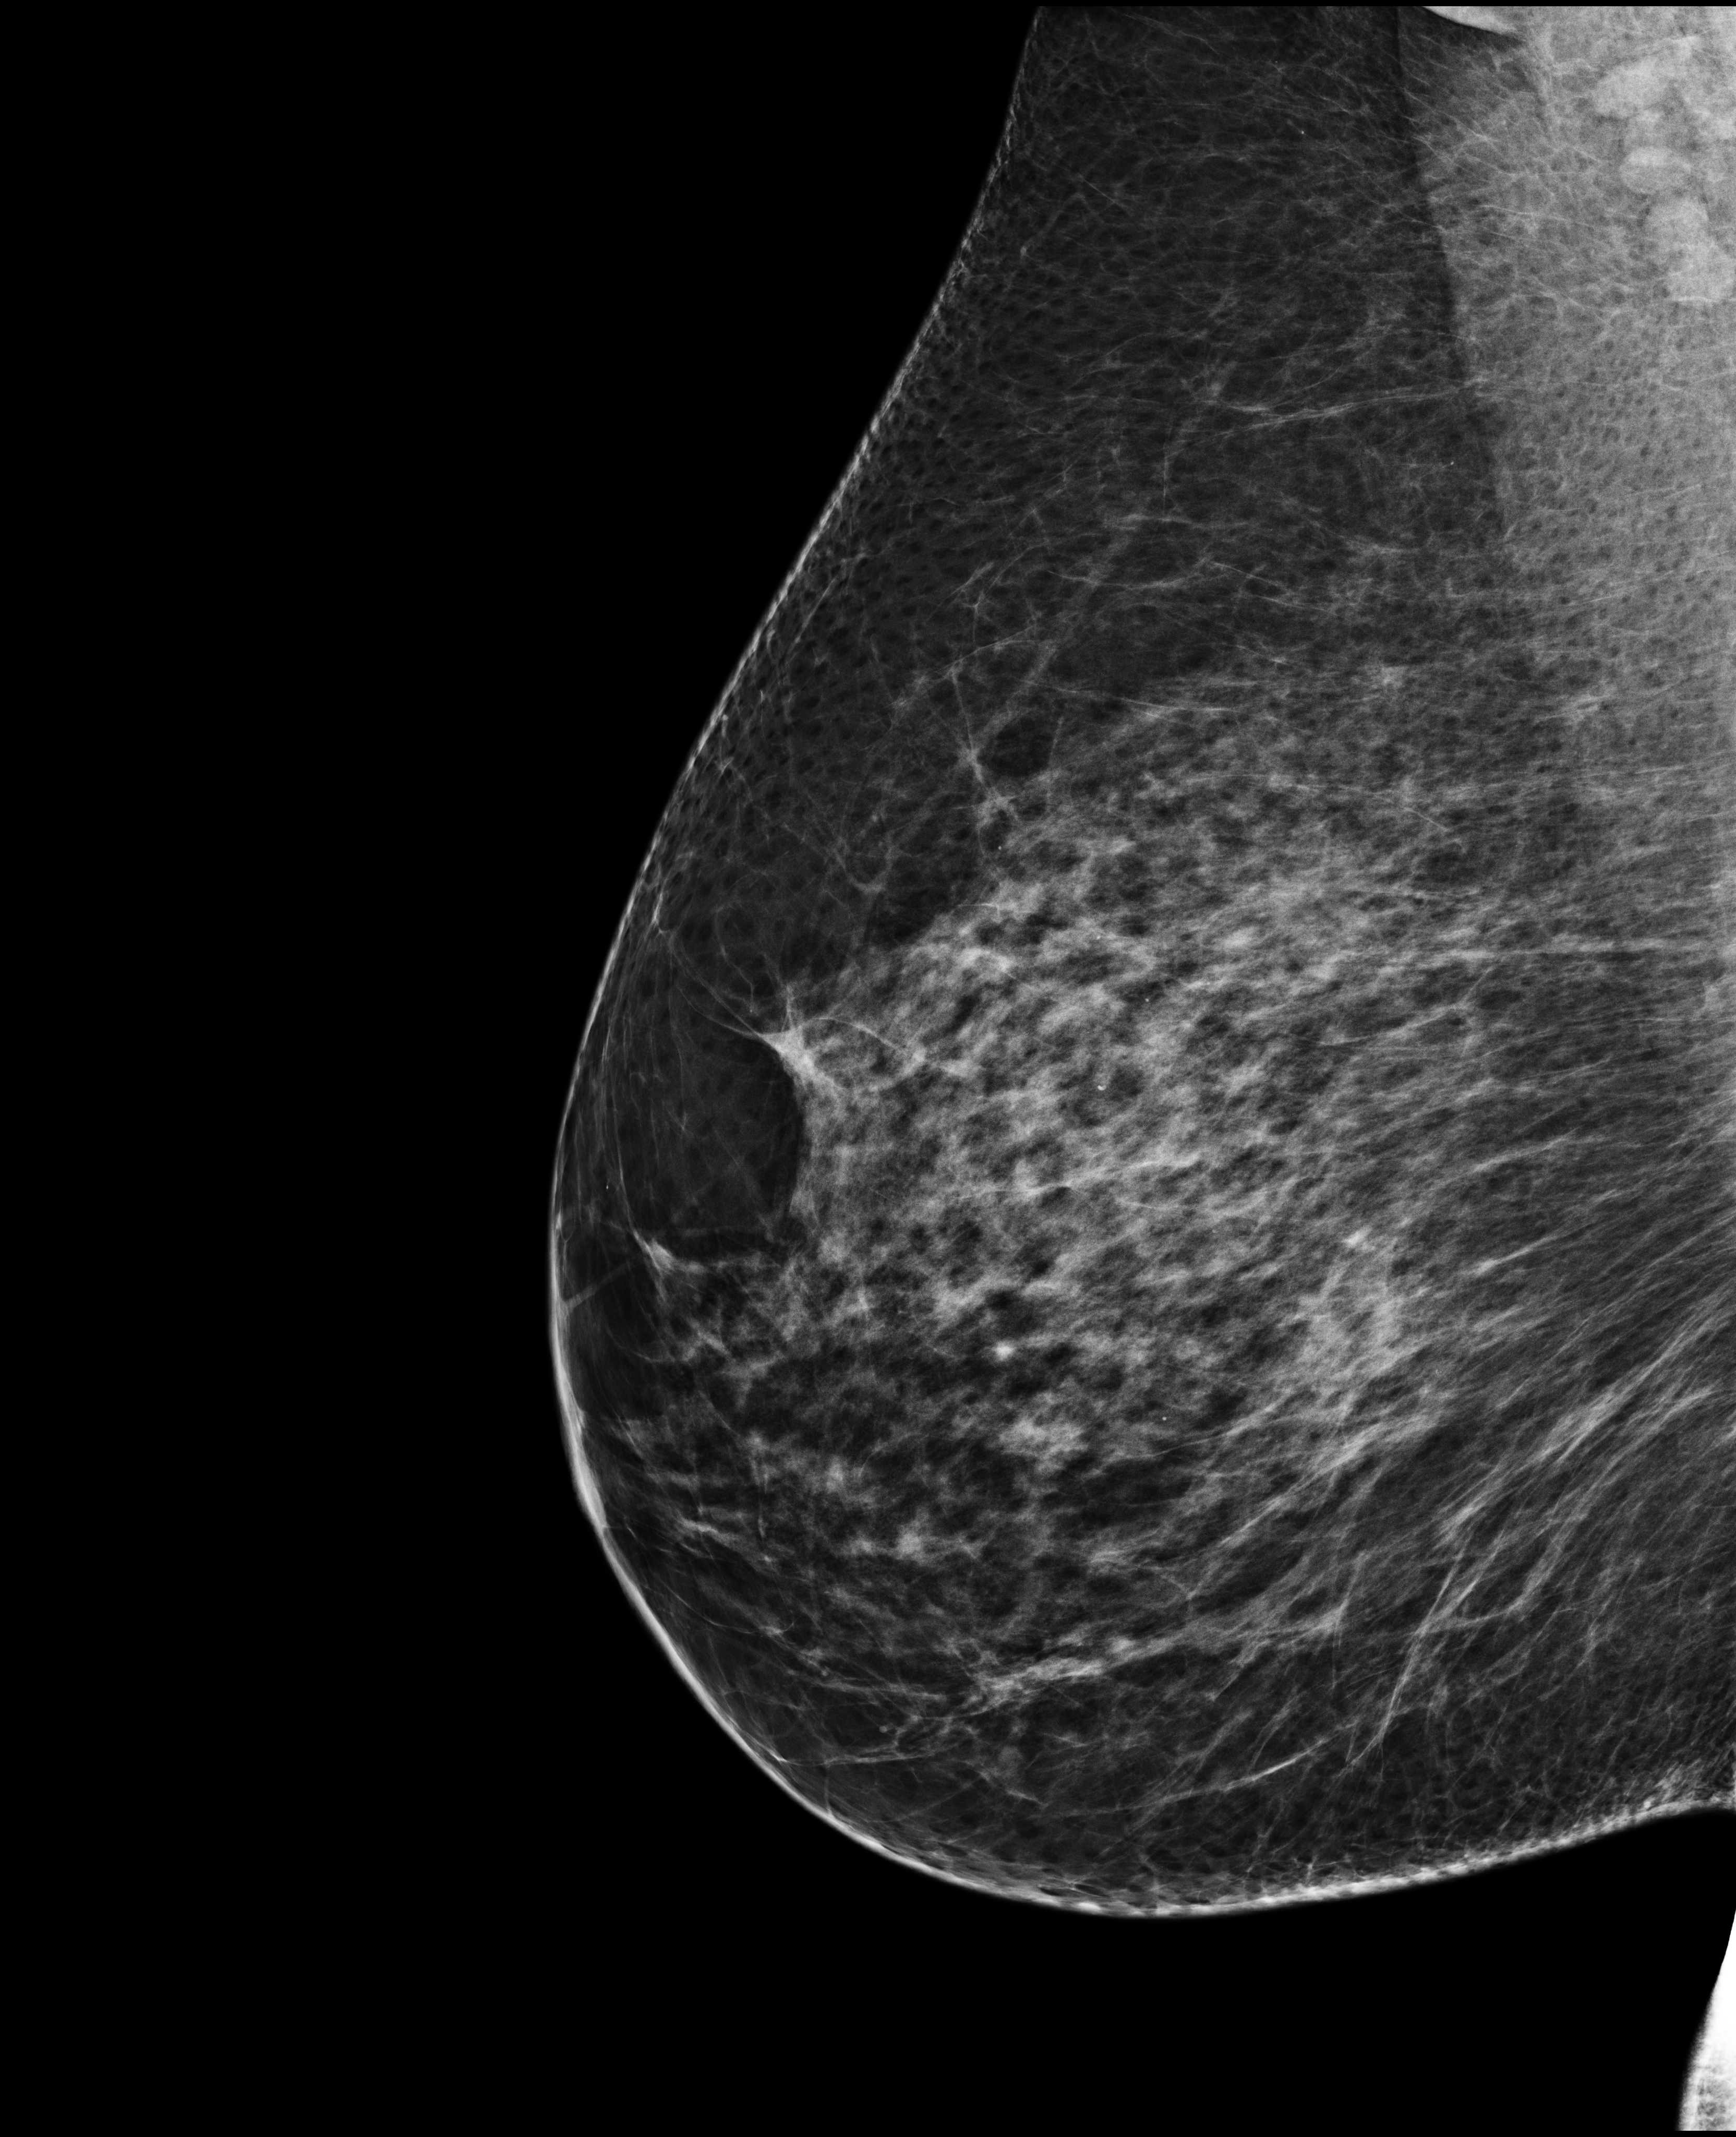
Full-field digital mammogram (FFDM), right breast, MLO view, diagnostic examination (additional views), compressed breast thickness 82 mm. Female patient, age 56 years.
- BI-RADS breast density category at the screening exam (both breasts, scale 1–4): 3
- final BI-RADS category for the screening round (tomosynthesis exam, both breasts): category 5
- recall: recalled for additional imaging after this screen